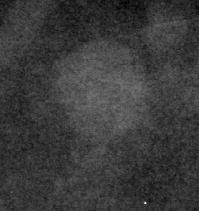
Crop from a digitized film mammogram around one marked abnormality; left breast; CC view.
Mass, shape lymph node, margins circumscribed; BI-RADS assessment category 3; subtlety rating 2 on a 1 (subtle) to 5 (obvious) scale; benign without callback (not worked up further).